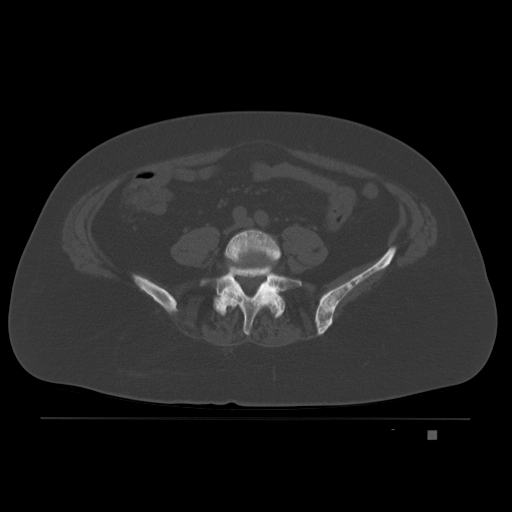
CT including the spine, one axial slice. Slice 34 of 221 in the series (ordered by position). Bone window (W 1800 / L 400 HU). 3 mm slice thickness. 512 × 512 image matrix, field of view 474 × 474 mm. Patient: female, 63 years. From the clinical record (not read from this slice): primary cancer: breast.
Structures marked on this image (semi-automatically segmented with operator editing):
- L4 vertebra: bounding box (x1, y1, x2, y2) in pixels: (224, 229, 281, 291)
- L5 vertebra: (200, 263, 299, 335)